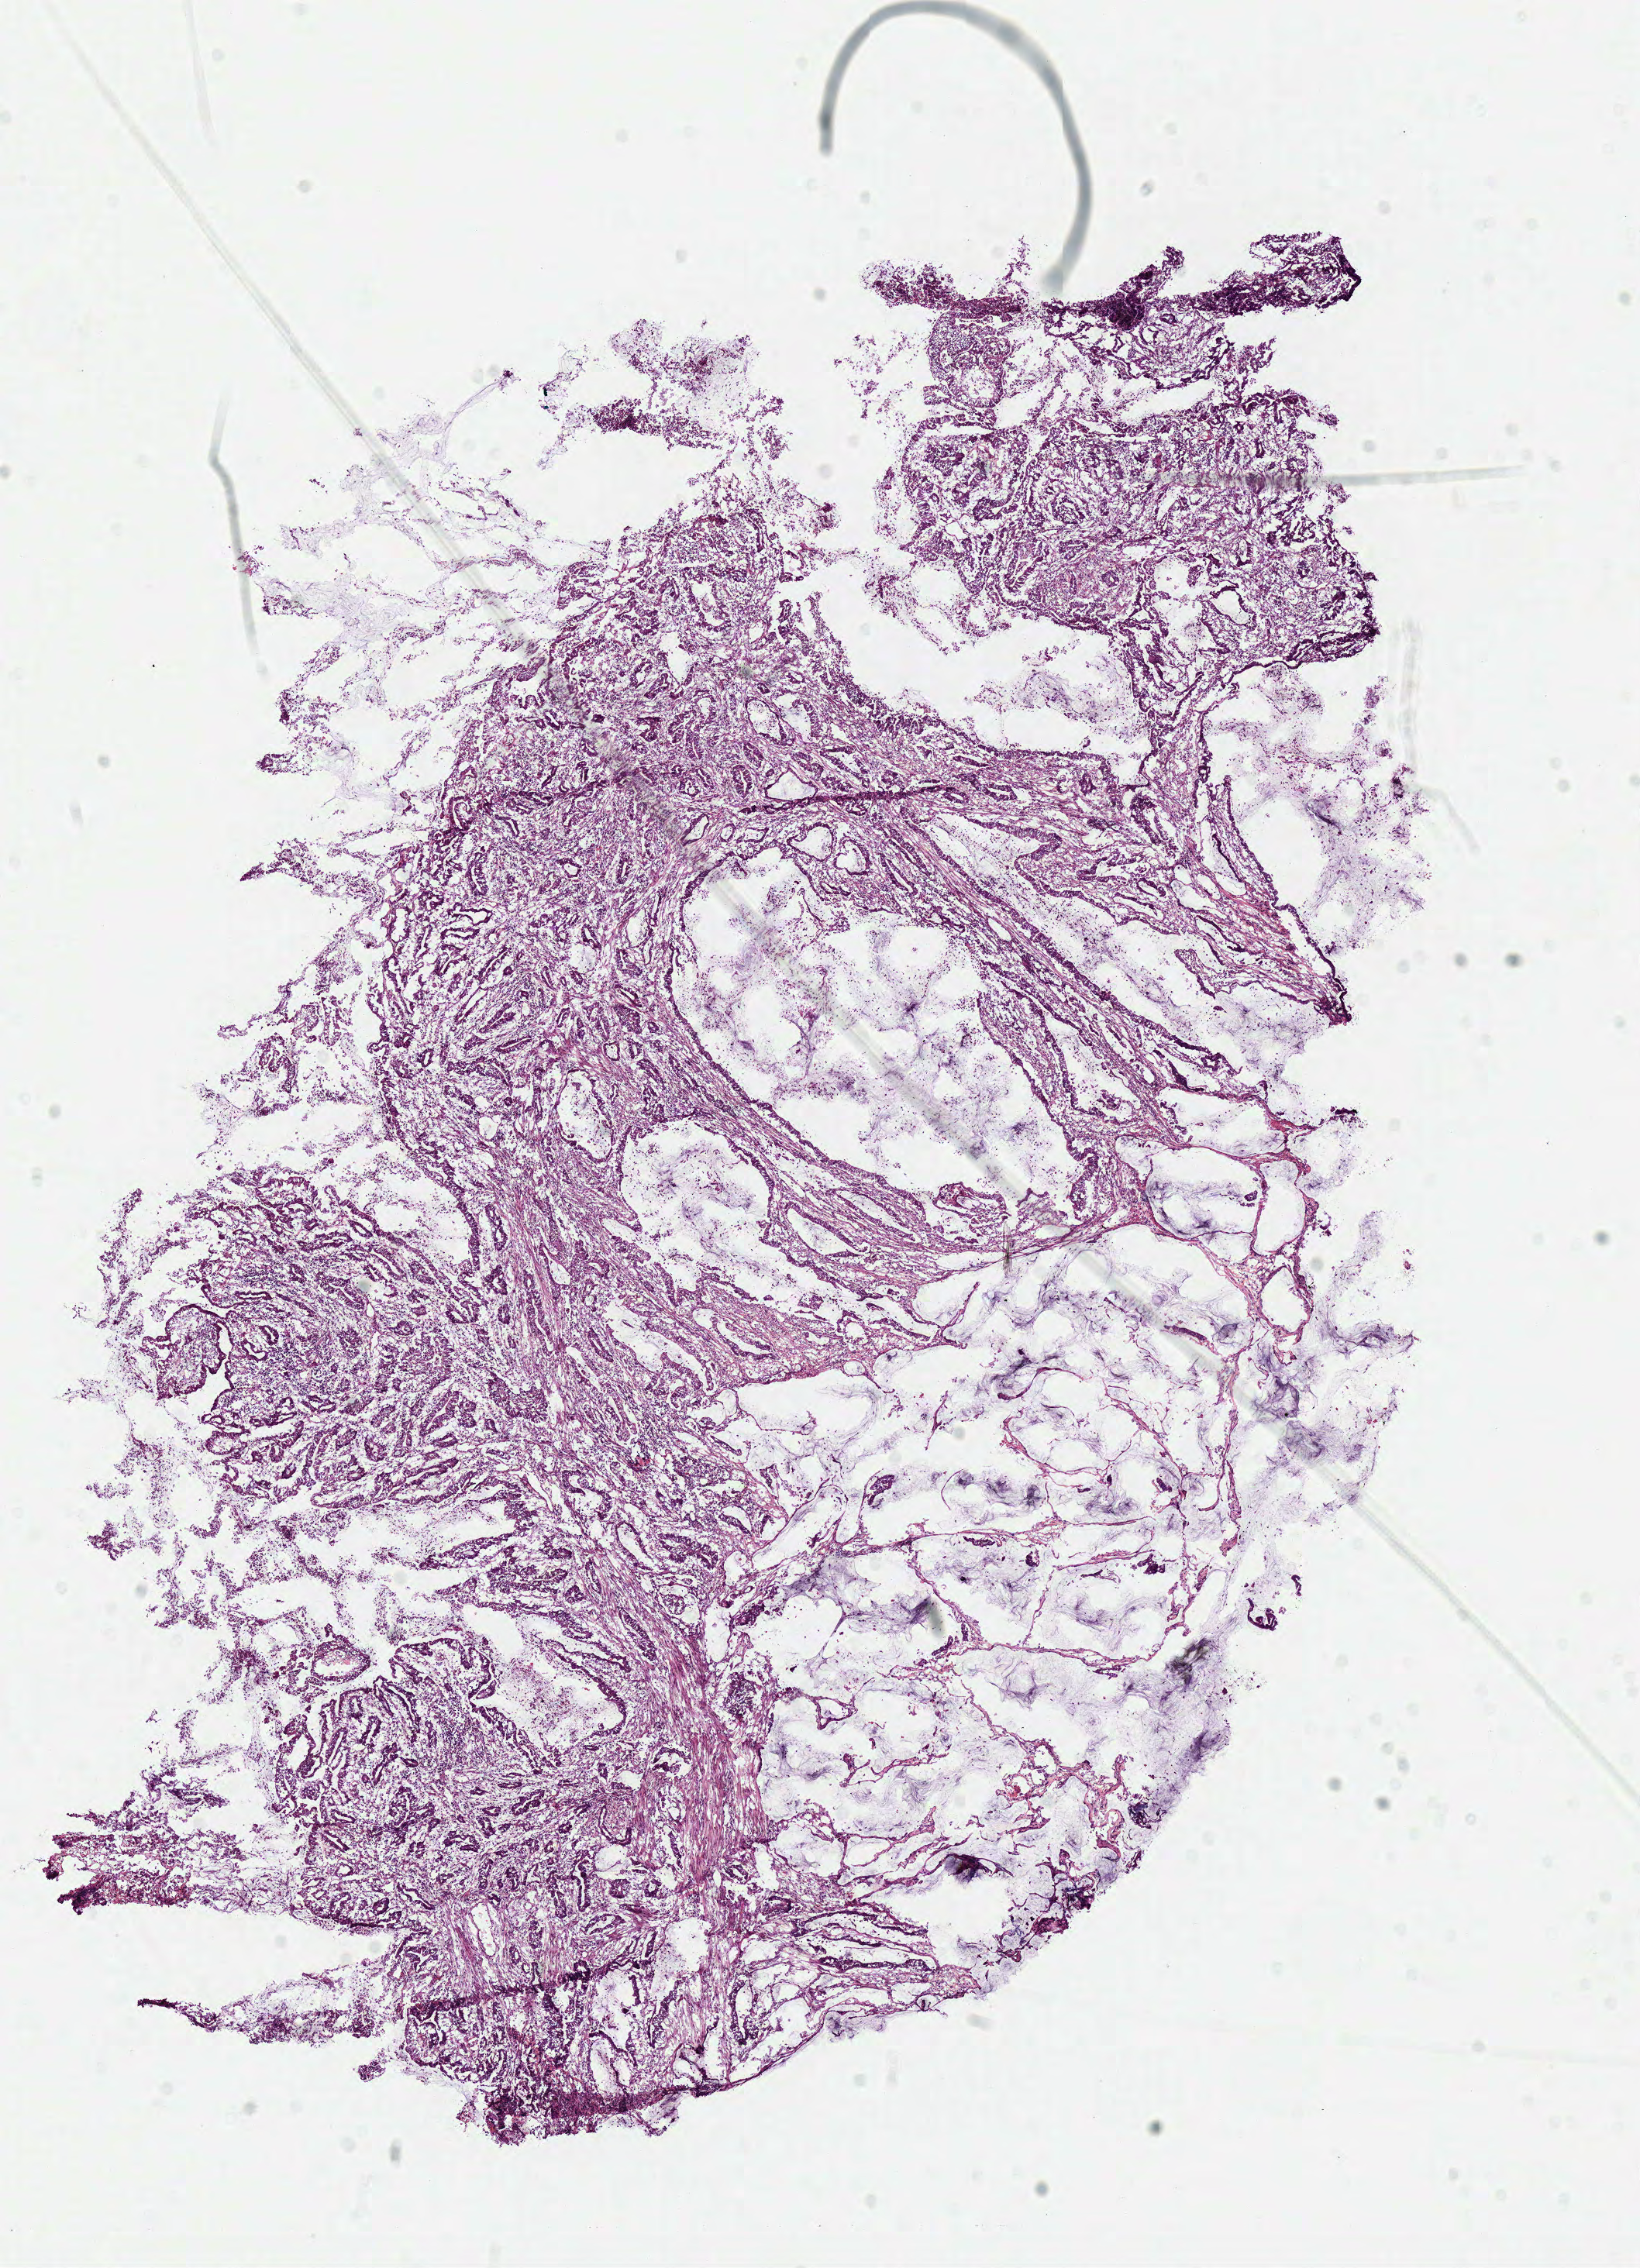
Whole-slide histology image, H&E-stained — whole scanned area (about 8.3 x 11.5 mm, acquisition: 40x scan) shown as a low-resolution overview, frozen section from the top of the tissue portion, colon, primary tumour sample. Patient sex: female. Composition of this section per pathologist review: tumour cells 77%, tumour nuclei 77%, normal cells 0%, stromal cells 20%, necrosis 3%.
AJCC pathologic stage: IIA (6th edition). Lymph nodes positive (case pathology): 0 of 15 examined. Diagnosis: Mucinous adenocarcinoma (cecum).